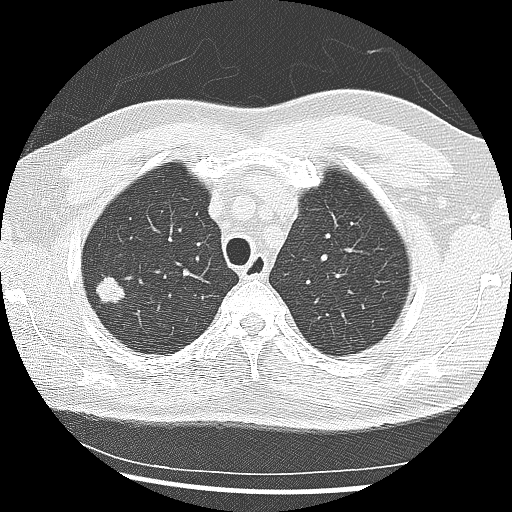
Low-dose screening chest CT, one axial slice. Slice 211 of 265 in the series (ordered by position). Lung window (W 1500 / L -600 HU). 2.5 mm slice thickness. 512 × 512 image matrix, field of view 340 × 340 mm.
Annotated regions visible in this slice (expert manual segmentation):
- lesion 1 (tumor, upper lobe of right lung): bounding box <96,277,124,303> (left, top, right, bottom; pixels)